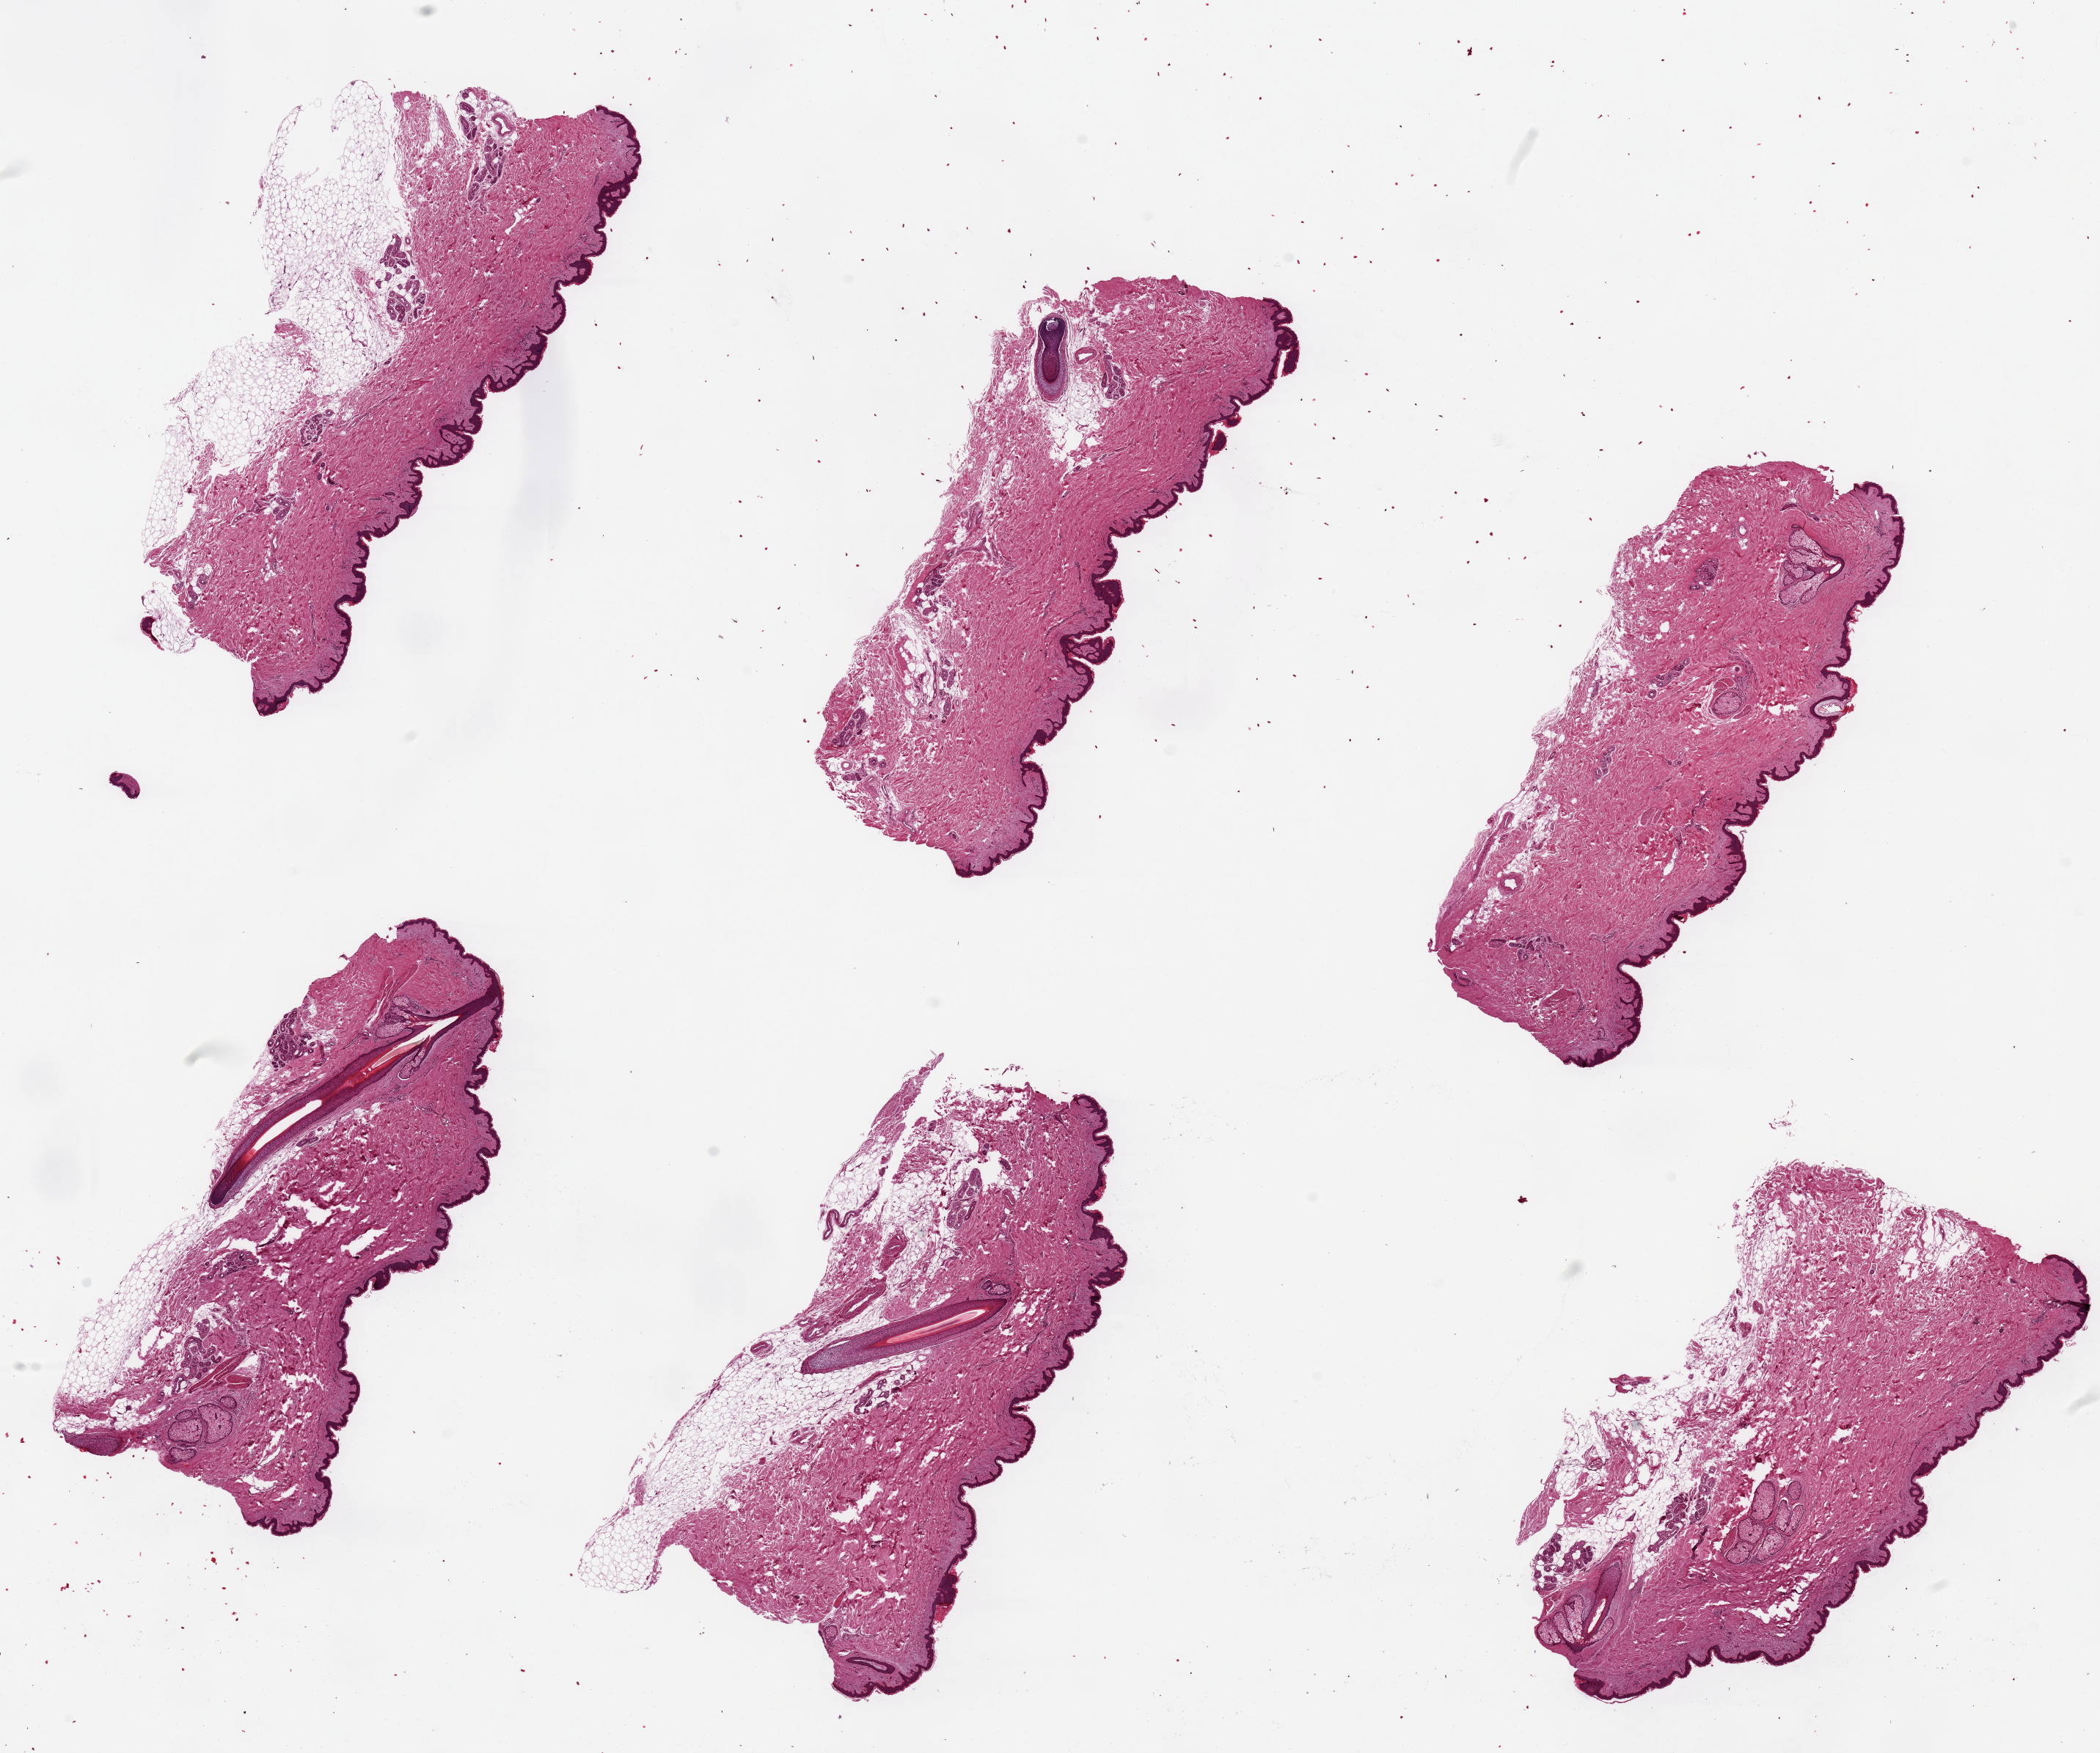
Hematoxylin and eosin (H&E) whole-slide image, whole scanned area (about 22.6 x 18.9 mm, slide scanned at 20x) shown as a low-resolution overview; PAXgene-fixed, paraffin-embedded tissue; sampled site (target tissue): skin of suprapubic region; tissue donor sample.
* pathologist's review note for this sample: 6 pieces ~7x2.5mm. Squamous epithelium is ~2% of thickness